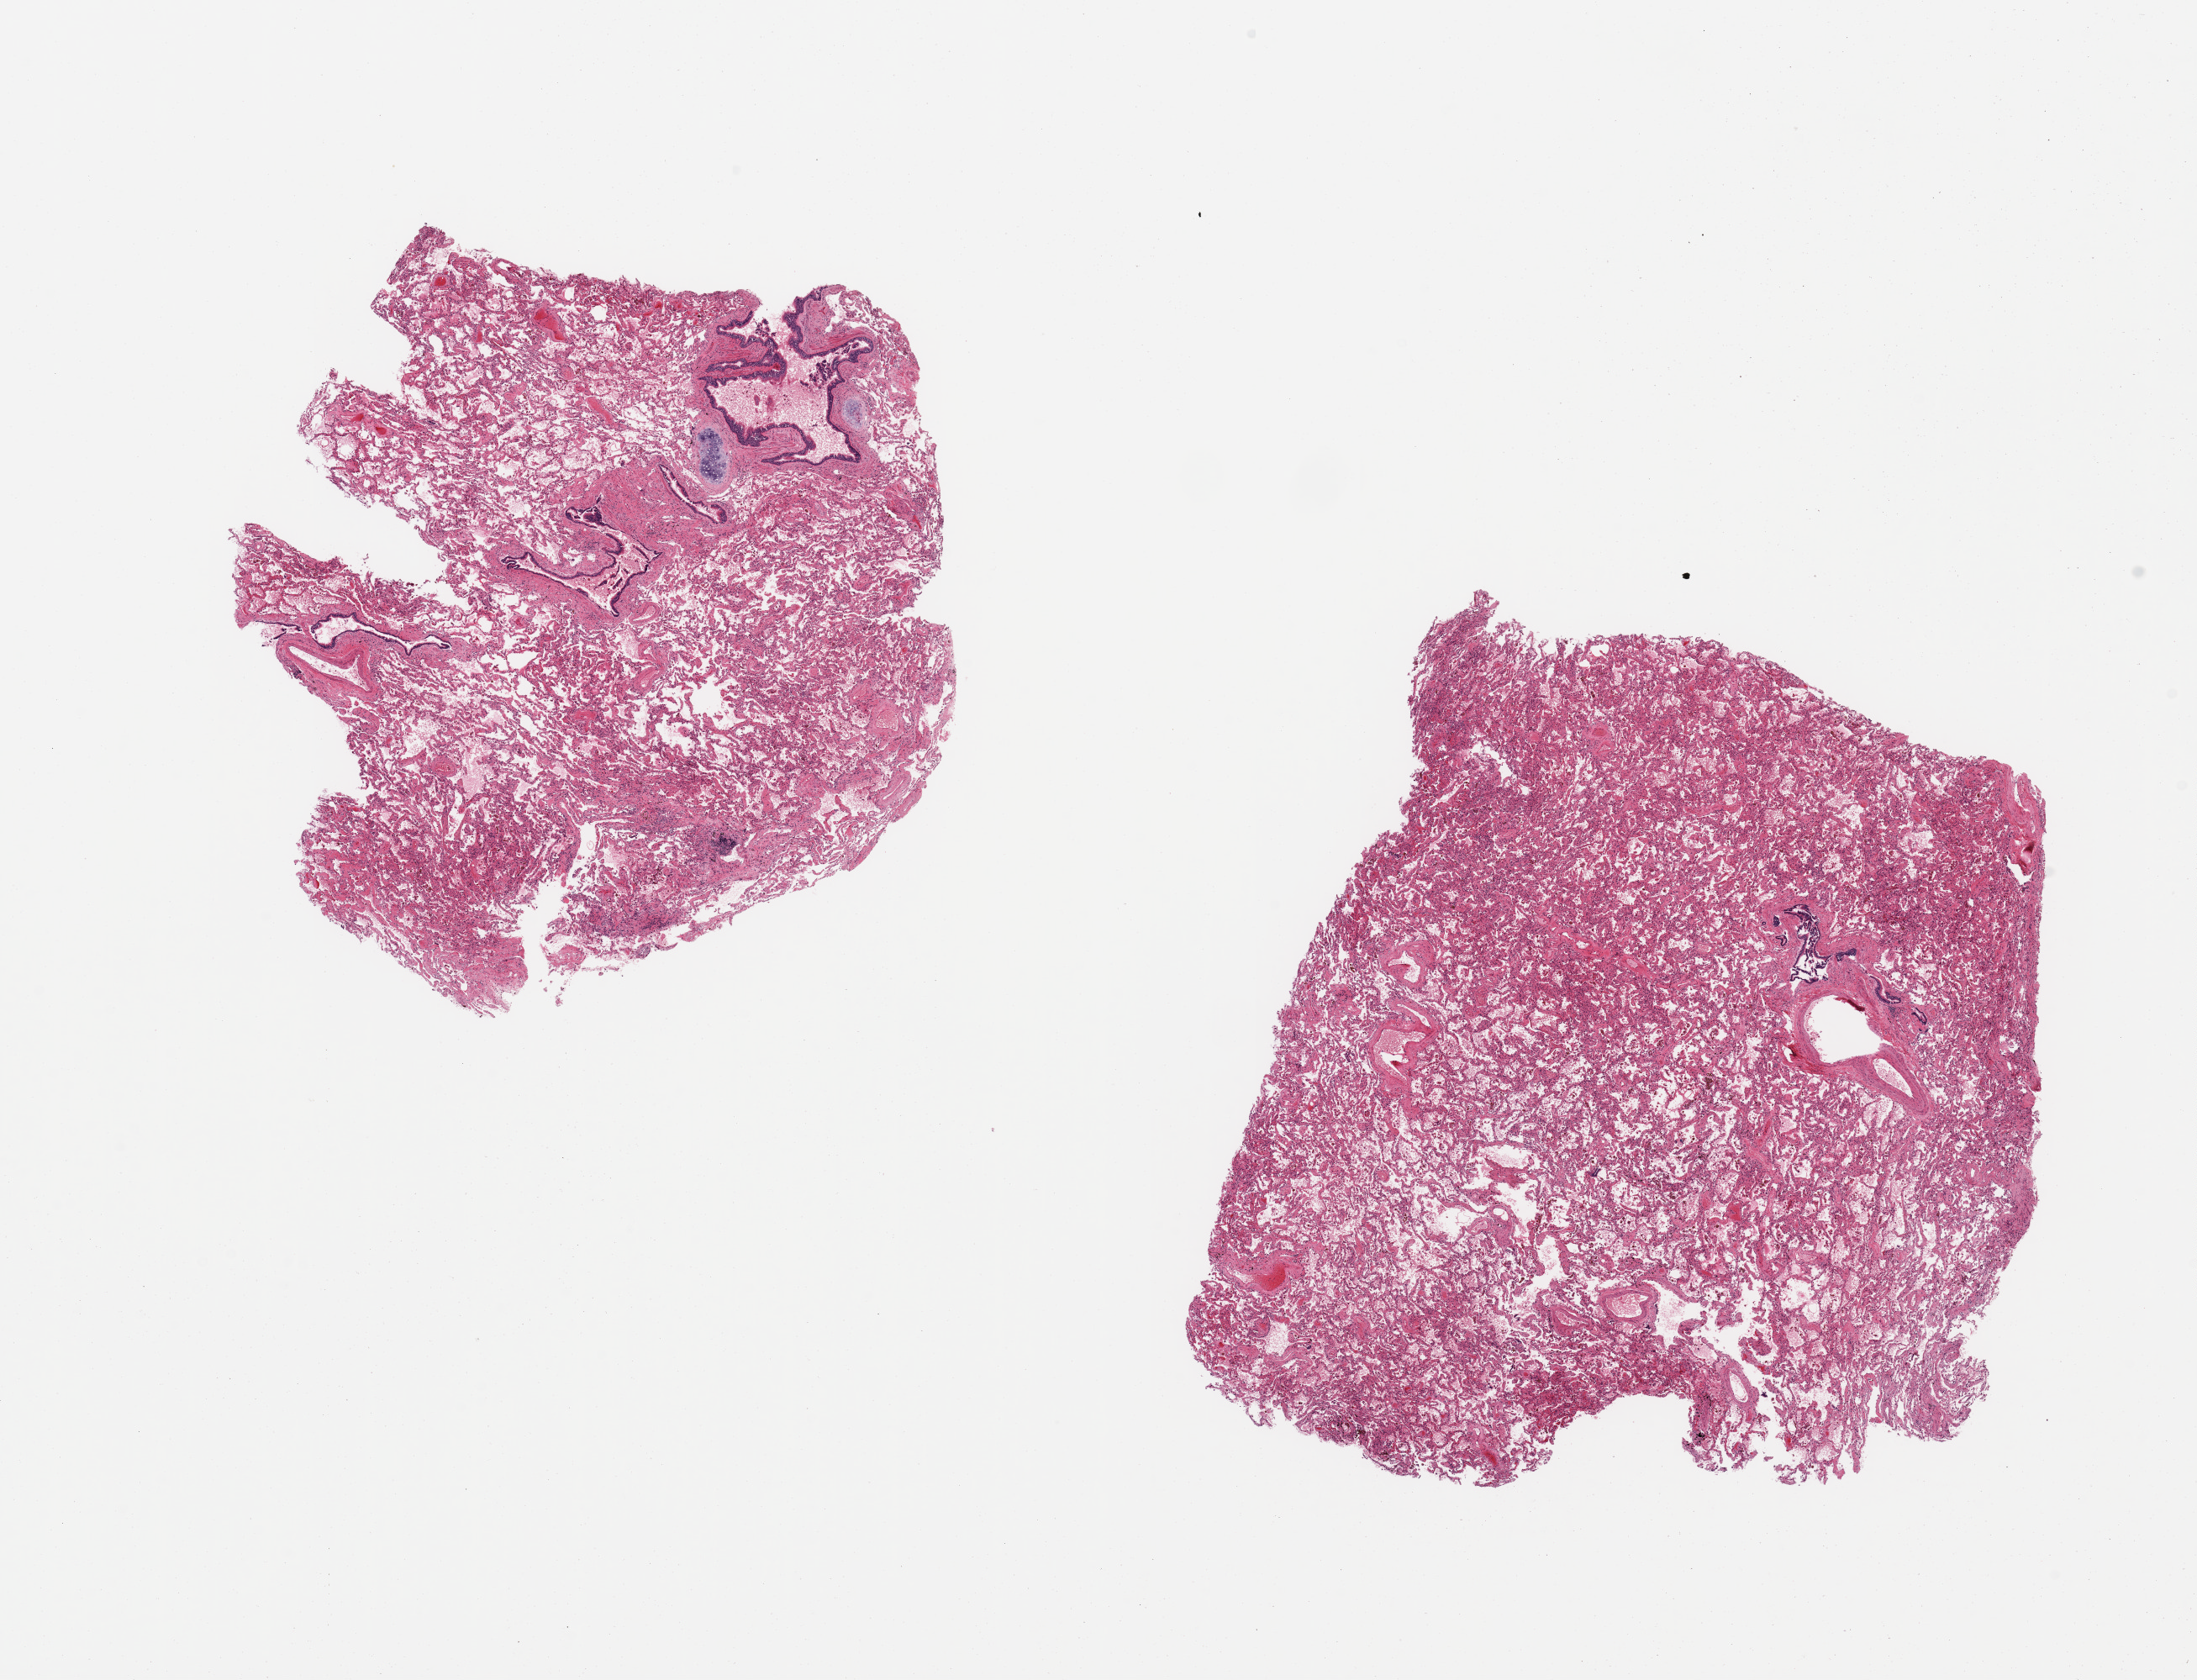
H&E whole-slide image, whole scanned area (about 20.7 x 15.8 mm, acquisition: 20x scan) shown as a low-resolution overview; PAXgene-fixed paraffin-embedded (PFPE) section; section of lung (target tissue); tissue donor sample. Male donor.
Review note (as recorded): 2 pieces of pulmonary tissue; mild to moderate autolysis; one section contains bronchus with cartilage and a few bronchioles; congestion.